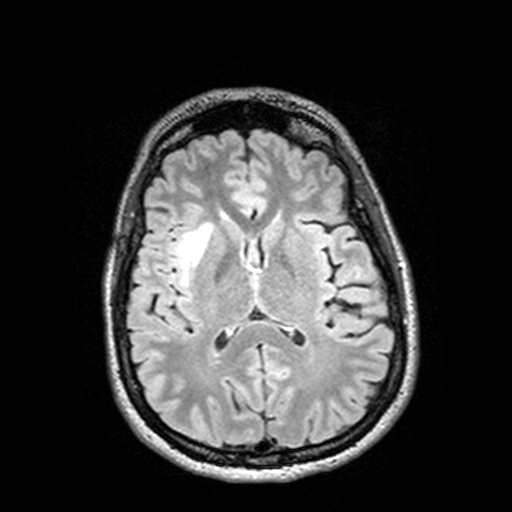
Brain MRI from a brain-tumour surgery series, one axial slice. Position 64 of 144 along the scan axis. T2 FLAIR. 1 mm slice thickness. 512 × 512 image matrix, field of view 250 × 250 mm. Case-level facts recorded for this patient, not image findings: histopathology: Astrocytoma; WHO grade: 3; IDH mutation: yes.
Structures marked on this image (expert manual segmentation):
- tumour: bounding box <194,226,228,280> (left, top, right, bottom; pixels)